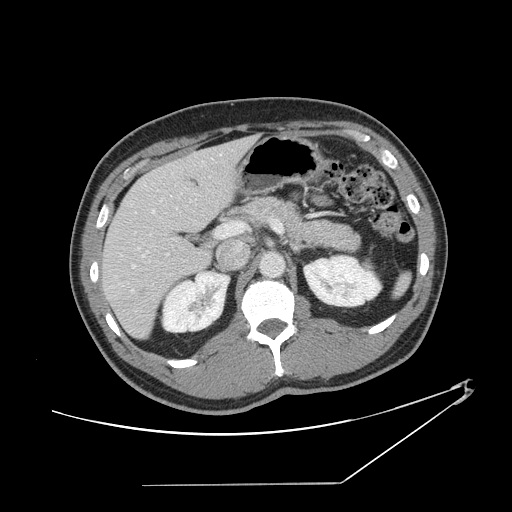
Contrast-enhanced abdominal CT, one axial slice. Position 78 of 152 along the scan axis. 120 kVp. Soft-tissue window (W 400 / L 40 HU). 2.5 mm slice thickness. 512 × 512 image matrix. Male patient, age 45 years. From the clinical record (not read from this slice): diagnosis: colorectal cancer liver metastases, imaged before liver resection; multiple liver metastases: no; largest metastasis: 1 cm.
Structures marked on this image (outlined manually by an expert reader):
- hepatic veins: box from (x=131, y=153) to (x=222, y=292) px
- liver: (x=103, y=138)–(x=254, y=338)
- planned liver remnant (the part of the liver to remain after resection): (x=103, y=157)–(x=214, y=338)
- portal vein (with intrahepatic branches): (x=132, y=220)–(x=283, y=268)